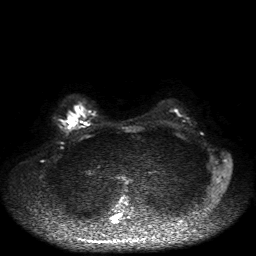
Breast MRI, one axial slice. Slice 31 of 50 in the series (ordered by position). Diffusion-weighted series; image 2 of 4 stored at this slice position (different b-values; order by instance number). 1.5 T. 4 mm slice thickness. 256 × 256 image matrix, field of view 360 × 360 mm. Female patient.
Annotated regions visible in this slice (manually delineated by an expert):
- tumour on diffusion-weighted imaging: box from (x=67, y=118) to (x=73, y=128) px